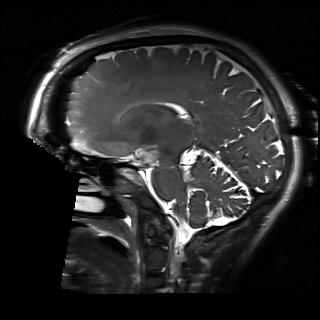
Brain MRI from a brain-tumour surgery series, one sagittal slice; slice 107 of 192 in the series (ordered by position); 1 mm slice thickness; 320 × 320 image matrix, field of view 230 × 230 mm. Case-level facts recorded for this patient, not image findings: histopathology: Glioblastoma; WHO grade: 2.
Outlined on this slice (outlined manually by an expert reader):
- residual tumour: bounding box [x1, y1, x2, y2] px = [136, 149, 158, 163]